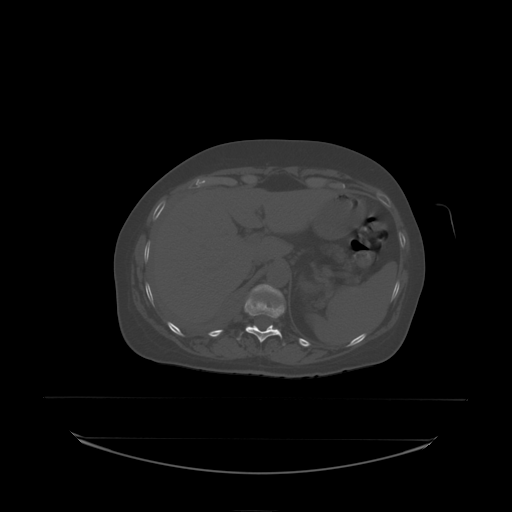
CT including the spine, one axial slice. Slice 102 of 242 in the series (ordered by position). Bone window (W 1800 / L 400 HU). 2.5 mm slice thickness. 512 × 512 image matrix, field of view 500 × 500 mm. Patient: female, 53 years. Case-level facts recorded for this patient, not image findings: primary cancer: lung.
Annotated regions visible in this slice (semi-automatically segmented with operator editing):
- T11 vertebra: box from (x=245, y=298) to (x=285, y=338) px
- T12 vertebra: (x=252, y=284)–(x=283, y=329)